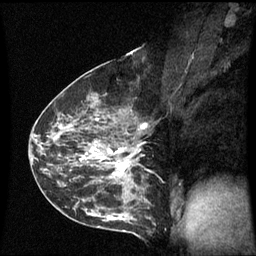
Breast MRI (dynamic contrast-enhanced), one sagittal slice. Position 34 of 60 along the scan axis. Dynamic contrast-enhanced series, image 2 of 3 at this slice position (ordered by acquisition). 1.5 T. TE 4.2 ms, TR 8.9 ms. 2.3 mm slice thickness. 256 × 256 image matrix. Patient: female, 43 years. From the clinical record (not read from this slice): setting: breast cancer imaged before/during neoadjuvant chemotherapy; receptor status: HER2-positive.
Structures marked on this image (semi-automatically segmented with operator editing):
- analysis volume of interest (the breast-tissue region the enhancement analysis was run in; not a lesion): bounding box [x1, y1, x2, y2] px = [56, 80, 148, 195]
- tumour enhancement mask (voxels above the 70 % enhancement threshold inside the analysis volume of interest): [81, 126, 146, 176]